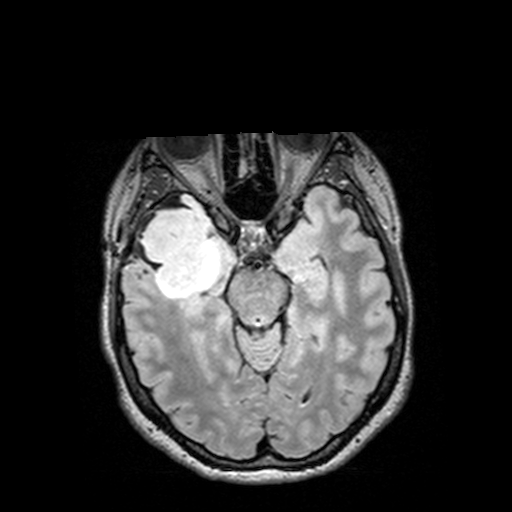
Brain MRI from a brain-tumour surgery series, one axial slice; position 89 of 144 along the scan axis; T2 FLAIR; 1 mm slice thickness; 512 × 512 image matrix. Case-level facts recorded for this patient, not image findings: histopathology: Astrocytoma; WHO grade: 3; IDH mutation: yes.
Outlined on this slice (expert manual segmentation):
- tumour: bounding box [x1, y1, x2, y2] px = [132, 193, 226, 308]